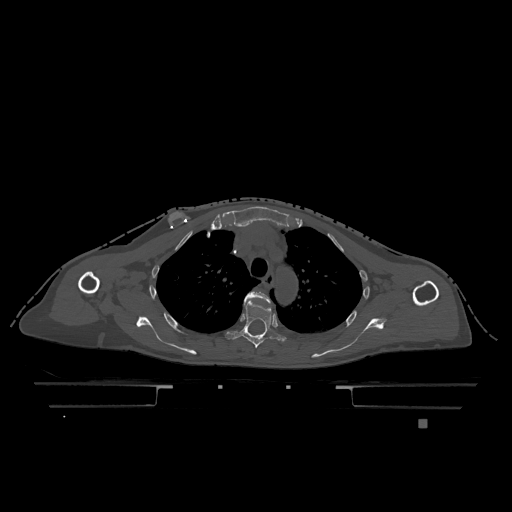
CT including the spine, one axial slice. Slice 887 of 1317 in the series (ordered by position). Bone window (W 1800 / L 400 HU). 0.5 mm slice thickness. 512 × 512 image matrix, field of view 500 × 500 mm. Patient: female, 74 years. Case-level facts recorded for this patient, not image findings: primary cancer: lung.
Annotated regions visible in this slice (semi-automatic segmentation, software-assisted and operator-edited):
- T3 vertebra: bounding box (x1, y1, x2, y2) in pixels: (244, 291, 270, 304)
- T4 vertebra: (225, 301, 287, 348)